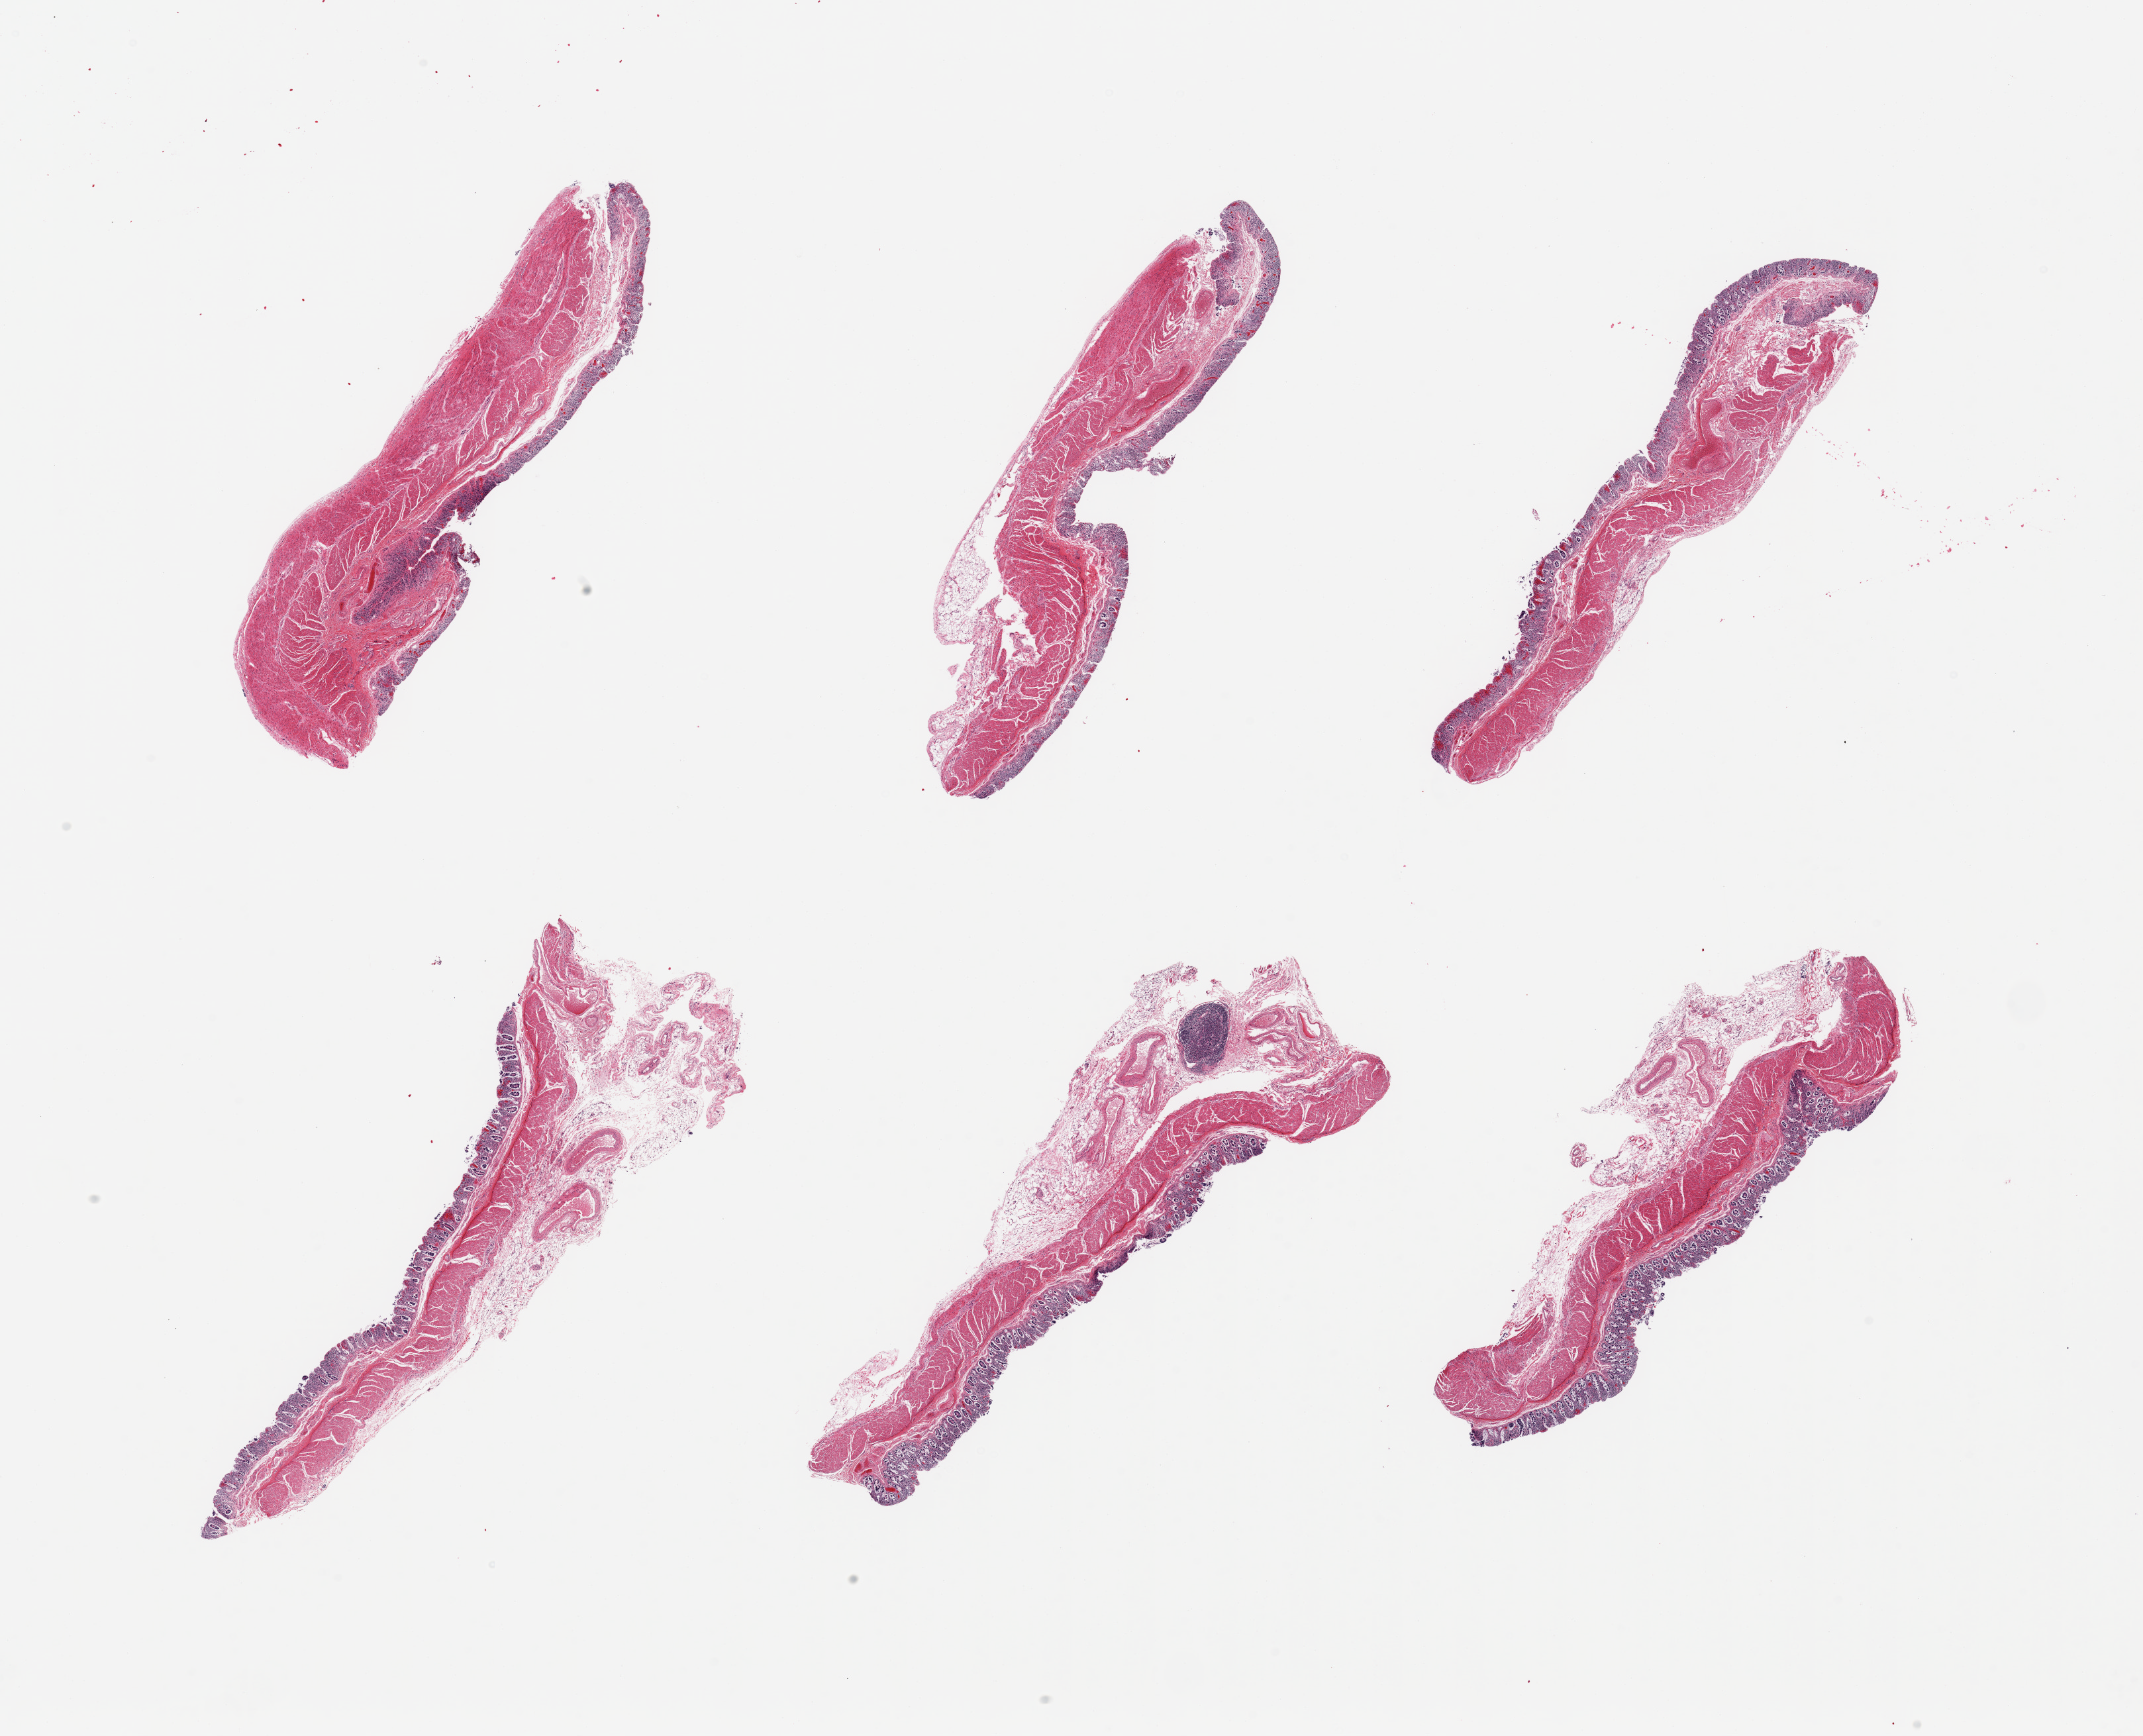
Digitized hematoxylin and eosin (H&E)-stained section — shown as a low-resolution overview of the whole scanned area (about 25.6 x 20.7 mm). PAXgene-fixed, paraffin-embedded tissue. Sampled site (target tissue): transverse colon. Donor tissue sample. Donor: male.
Pathologist's review note for this sample: 6 pieces; mucosa mostly autolysis=3; muscle =1.